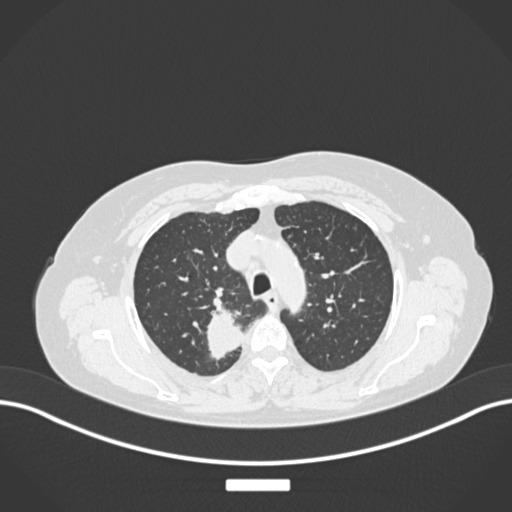
Chest CT, one axial slice. Slice 195 of 237 in the series (ordered by position). Lung window (W 1500 / L -600 HU). 1 mm slice thickness. 512 × 512 image matrix. Female patient, age 62 years. Case-level facts recorded for this patient, not image findings: clinical TNM (as recorded): T1c N1 M0.
Structures marked on this image (bounding box drawn by a radiologist):
- lung tumour (recorded histology: squamous cell carcinoma): bounding box [x1, y1, x2, y2] px = [202, 306, 246, 363]